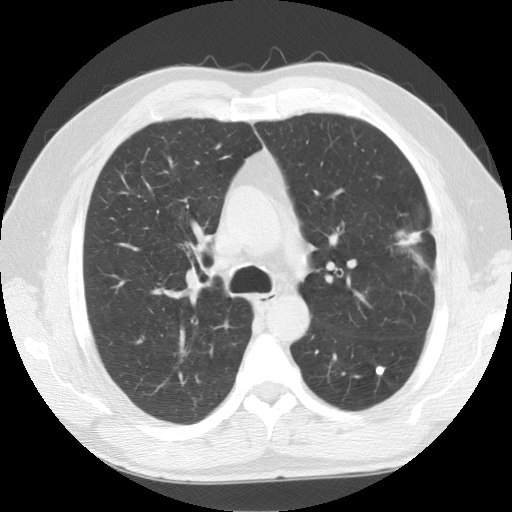
Chest CT (low-dose screening protocol), one axial image, baseline annual screen, lung window (W 1500 / L -600 HU), 2.5 mm slice thickness, slice 45 of 141 in the series, 512 × 512 image matrix. Male participant, aged 59 years at enrolment. Former smoker at enrolment.
Expert-annotated lung lesion, bounding box (x1, y1, x2, y2) in pixels: (371, 204, 453, 282). Screening reader's record for this exam (one nodule recorded; not confirmed to be the boxed lesion): non-calcified nodule or mass ≥4 mm, left upper lobe, 23 × 23 mm, spiculated (stellate) margins, soft tissue attenuation. Later outcome: lung cancer diagnosed 28 days after this screen — squamous cell carcinoma, NOS, left upper lobe, moderately differentiated (G2), stage IA (AJCC 6th edition), 27 mm at pathology.